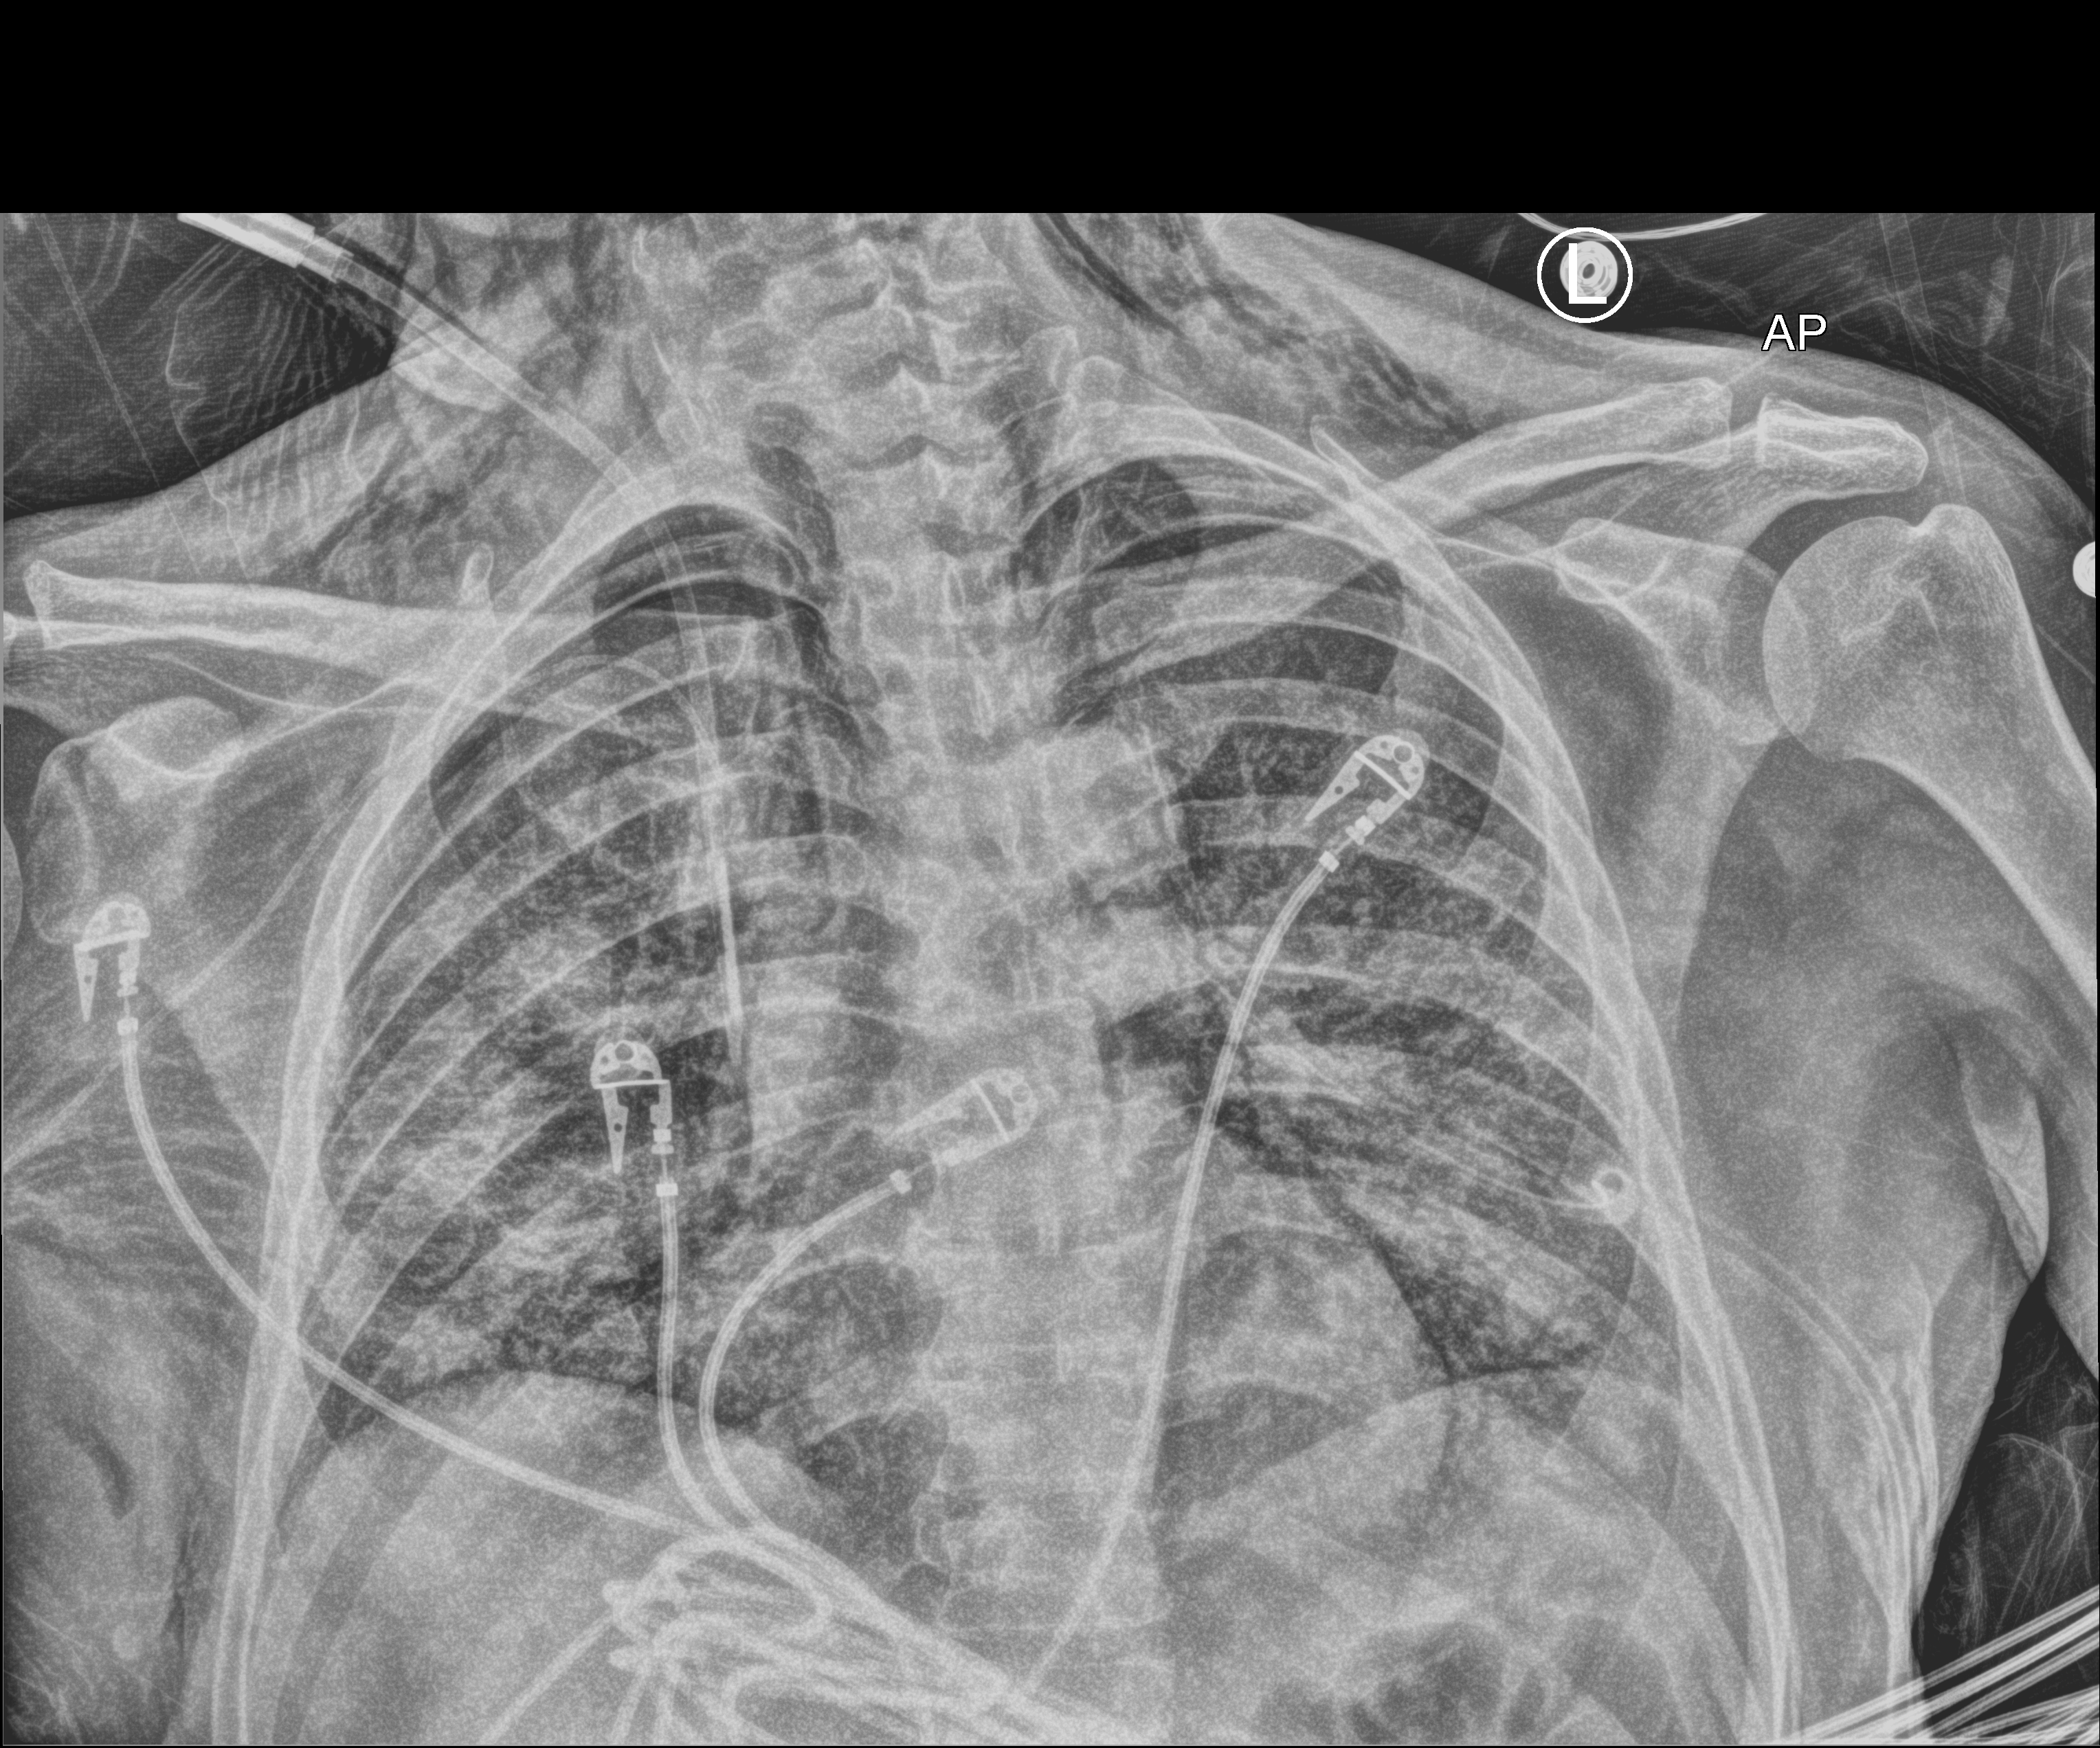
Bedside chest radiograph (computed radiography), anteroposterior (AP) projection. Patient hospitalised with COVID-19; male, aged 18–59 years.
From the hospital-stay record, not from the radiograph (when in the stay this image was taken is not recorded):
- mechanically ventilated during this hospital stay: yes
- length of hospital stay: 77 days